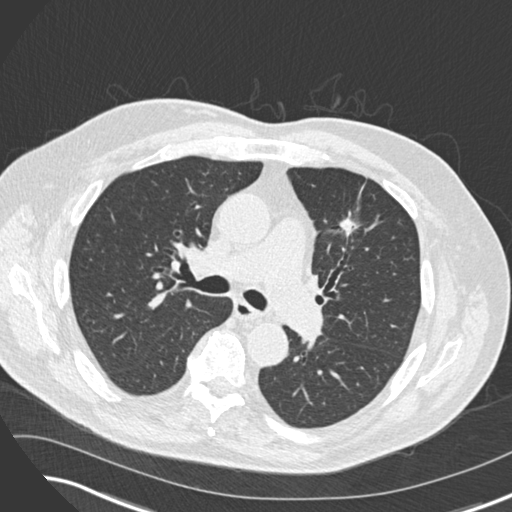
Low-dose screening chest CT, one axial slice; slice 102 of 169 in the series (ordered by position); reconstruction kernel B30f; lung window (W 1500 / L -600 HU); 2 mm slice thickness; 512 × 512 image matrix.
Outlined on this slice (outlined manually by an expert reader):
- lesion 1 (tumor, upper lobe of left lung): bounding box <340,213,358,237> (left, top, right, bottom; pixels)